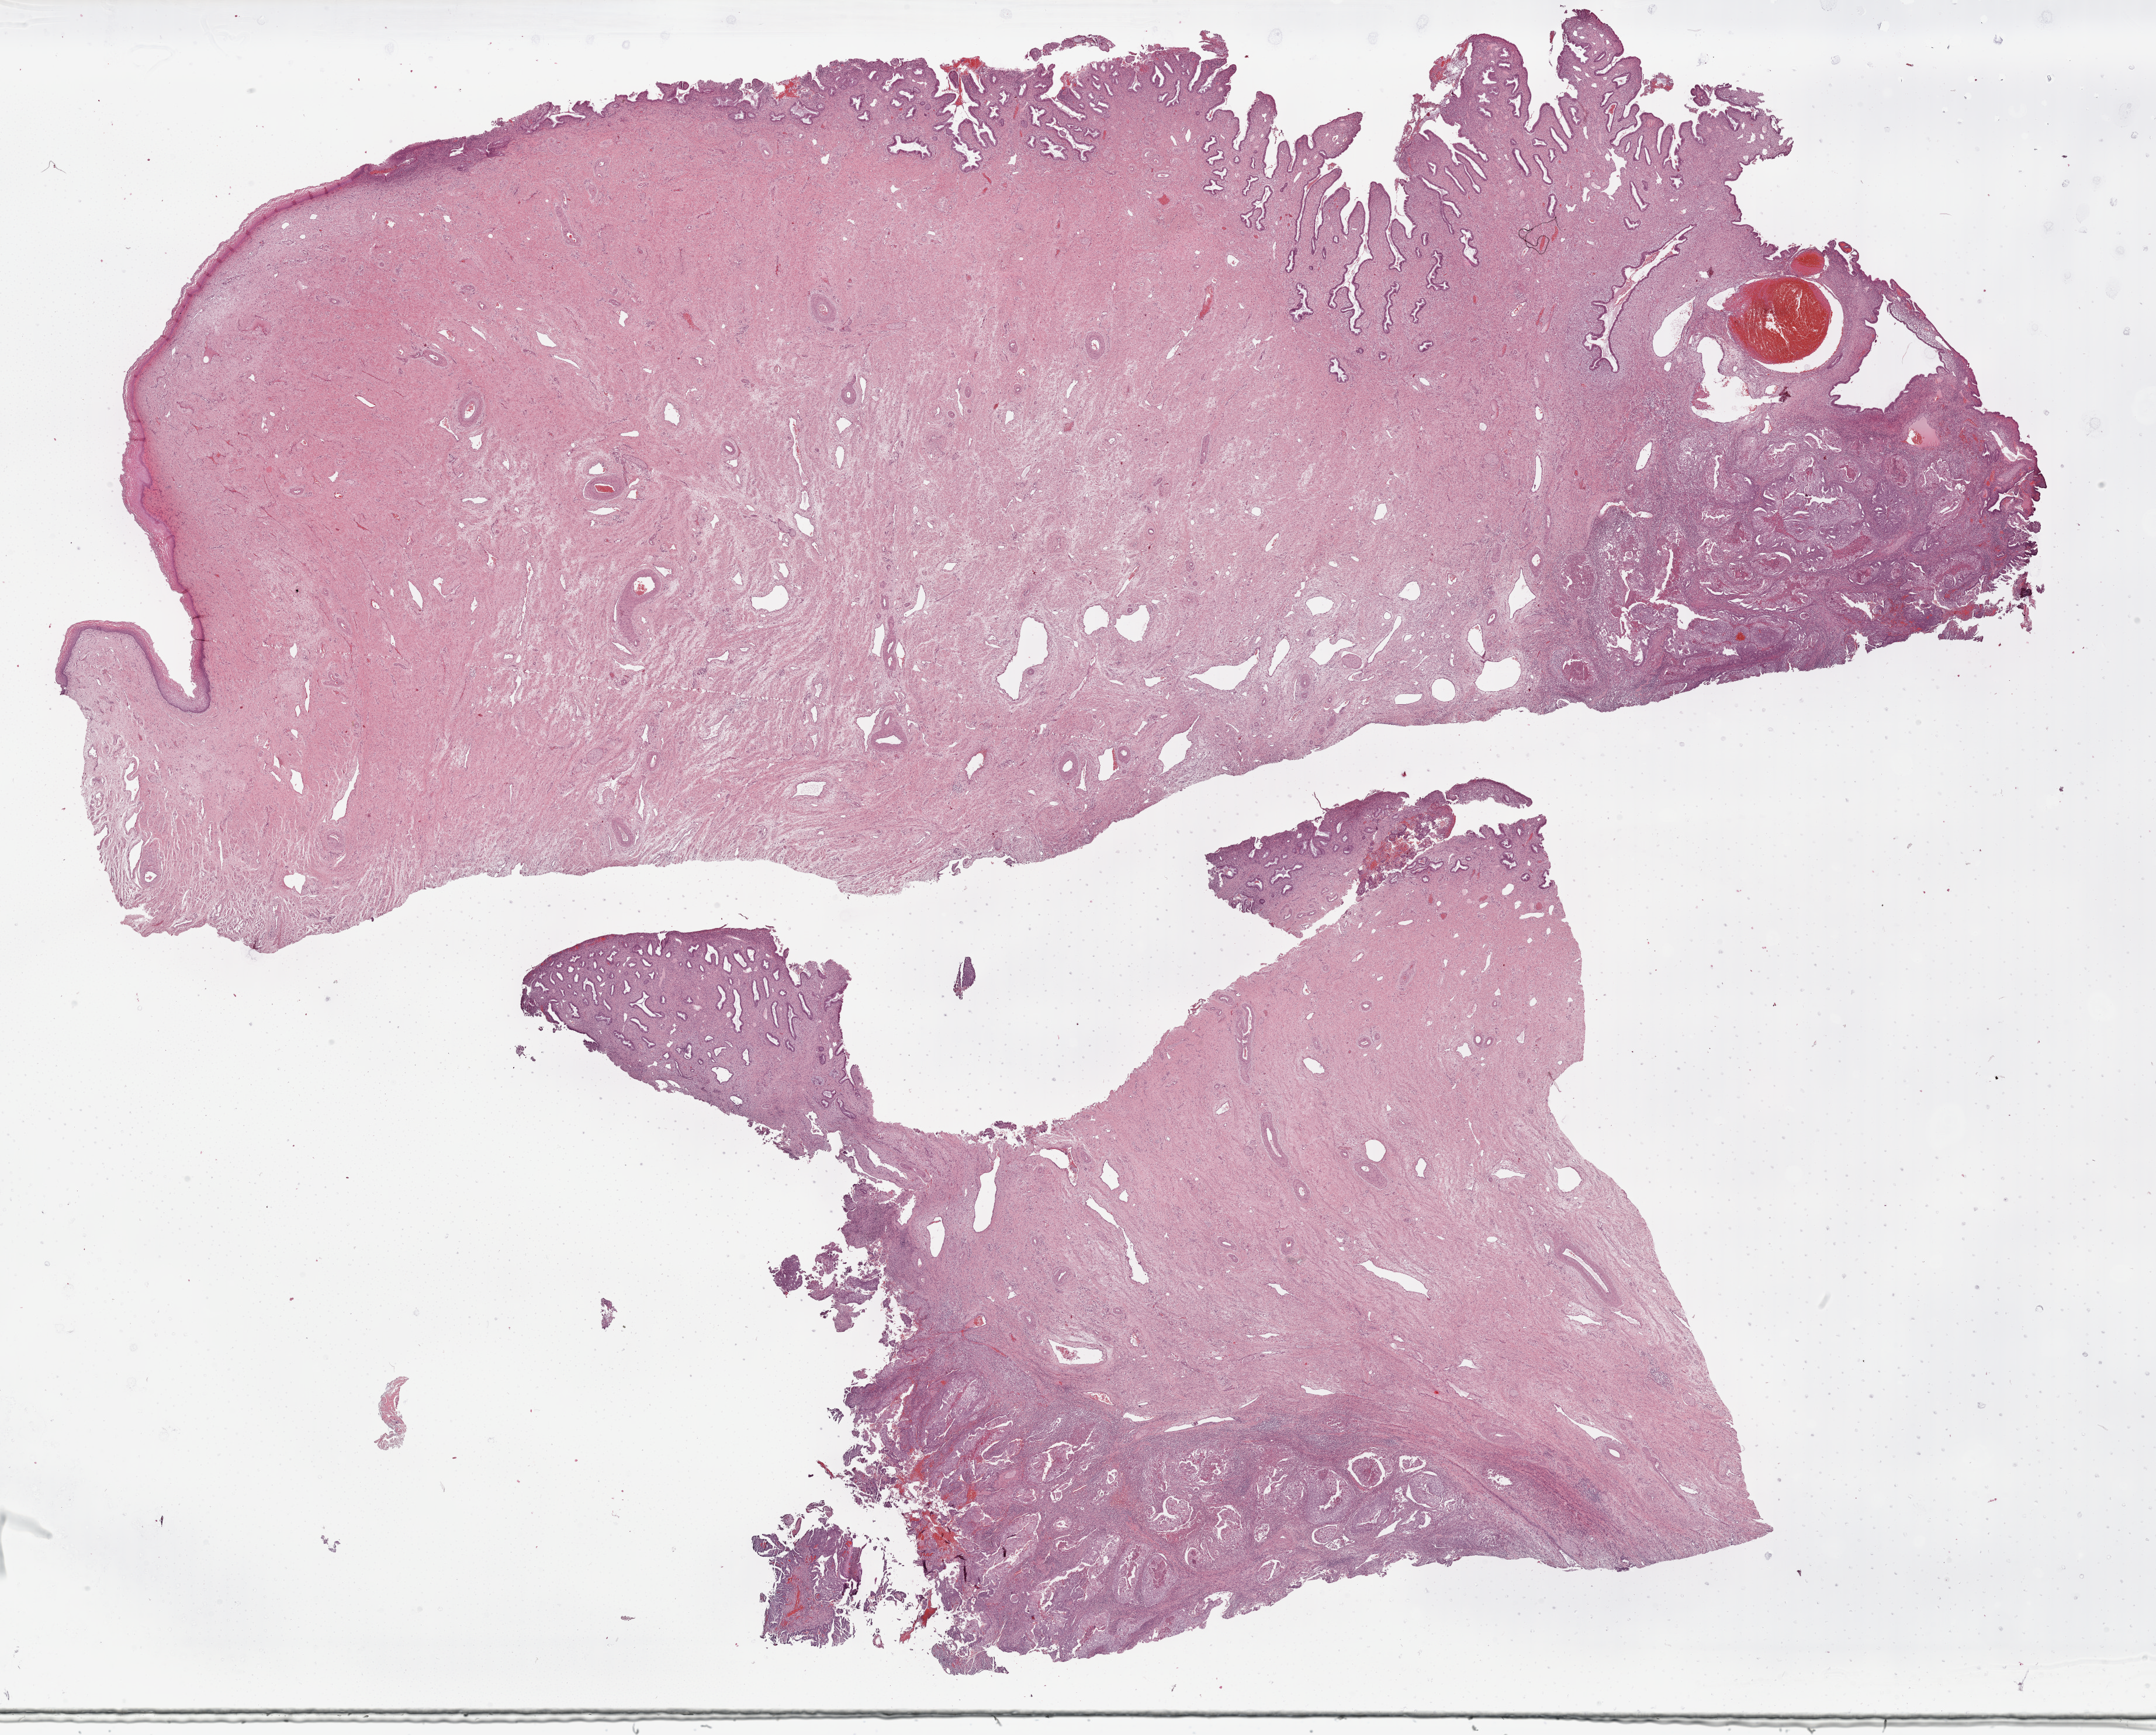
H&E whole-slide image, a low-resolution overview of the entire scanned area, about 29.1 x 23.4 mm, formalin-fixed paraffin-embedded (FFPE) diagnostic section, sample: primary tumour, uterus. Patient: female, age at initial diagnosis 39 years. Histologic grade: G3 (poorly differentiated).
* FIGO stage: IVB
* lymph nodes positive (case pathology): 1 of 2 examined
* pathologic diagnosis: Endometrioid adenocarcinoma, NOS (endometrium)